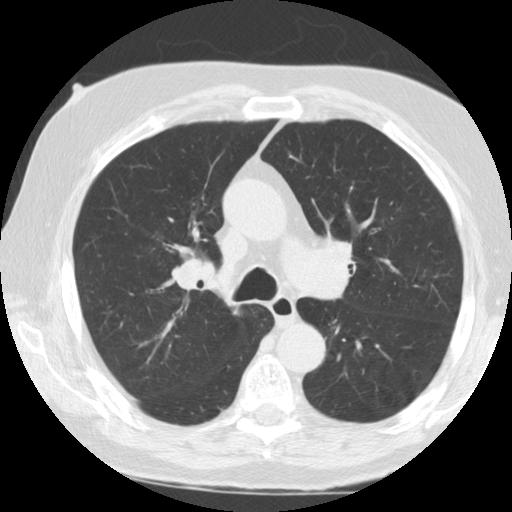
Chest CT (low-dose screening protocol), one axial image; second annual screen; lung window (W 1500 / L -600 HU); 2.5 mm slice thickness; standard (soft-tissue) reconstruction kernel (STANDARD); 512 × 512 image matrix, field of view 340 × 340 mm. Male participant, aged 72 years at enrolment. Former smoker at enrolment.
• Expert reader's lesion annotation, bounding box (x1, y1, x2, y2) in pixels: (159, 235, 227, 306).
• No non-calcified nodule or mass ≥4 mm was recorded by the screening reader at this exam.
• Official screen result: negative screen, minor abnormalities not suspicious for lung cancer.